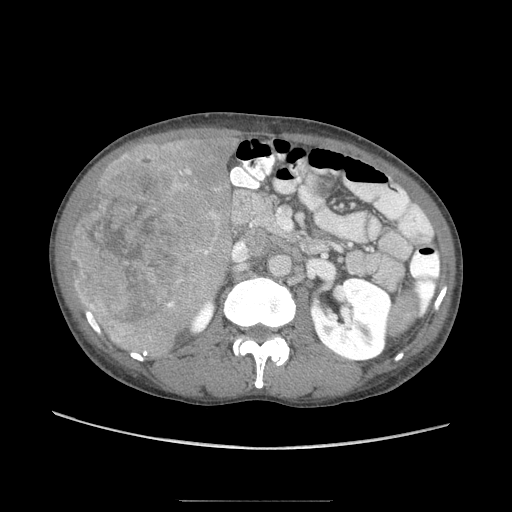
Contrast-enhanced abdominal CT (liver protocol), one axial slice. Slice 30 of 103 in the series (ordered by position). Reconstruction kernel STANDARD. Soft-tissue window (W 400 / L 40 HU). 2.5 mm slice thickness. 512 × 512 image matrix, field of view 380 × 380 mm. From the clinical record (not read from this slice): diagnosis: hepatocellular carcinoma (patient treated with transarterial chemoembolisation; whether this scan precedes or follows treatment is not stated here); TNM stage (as recorded): Stage-IIIA; Child-Pugh class: A; tumour differentiation: moderately differentiated; tumour nodularity: multinodular.
Outlined on this slice (semi-automatic segmentation, software-assisted and operator-edited):
- liver parenchyma outside the tumour (the mass and vessels are separate outlines, so this box may not span the whole liver): box from (x=78, y=130) to (x=236, y=357) px
- mass: (x=67, y=141)–(x=220, y=344)
- liver vessels: (x=144, y=352)–(x=147, y=355)